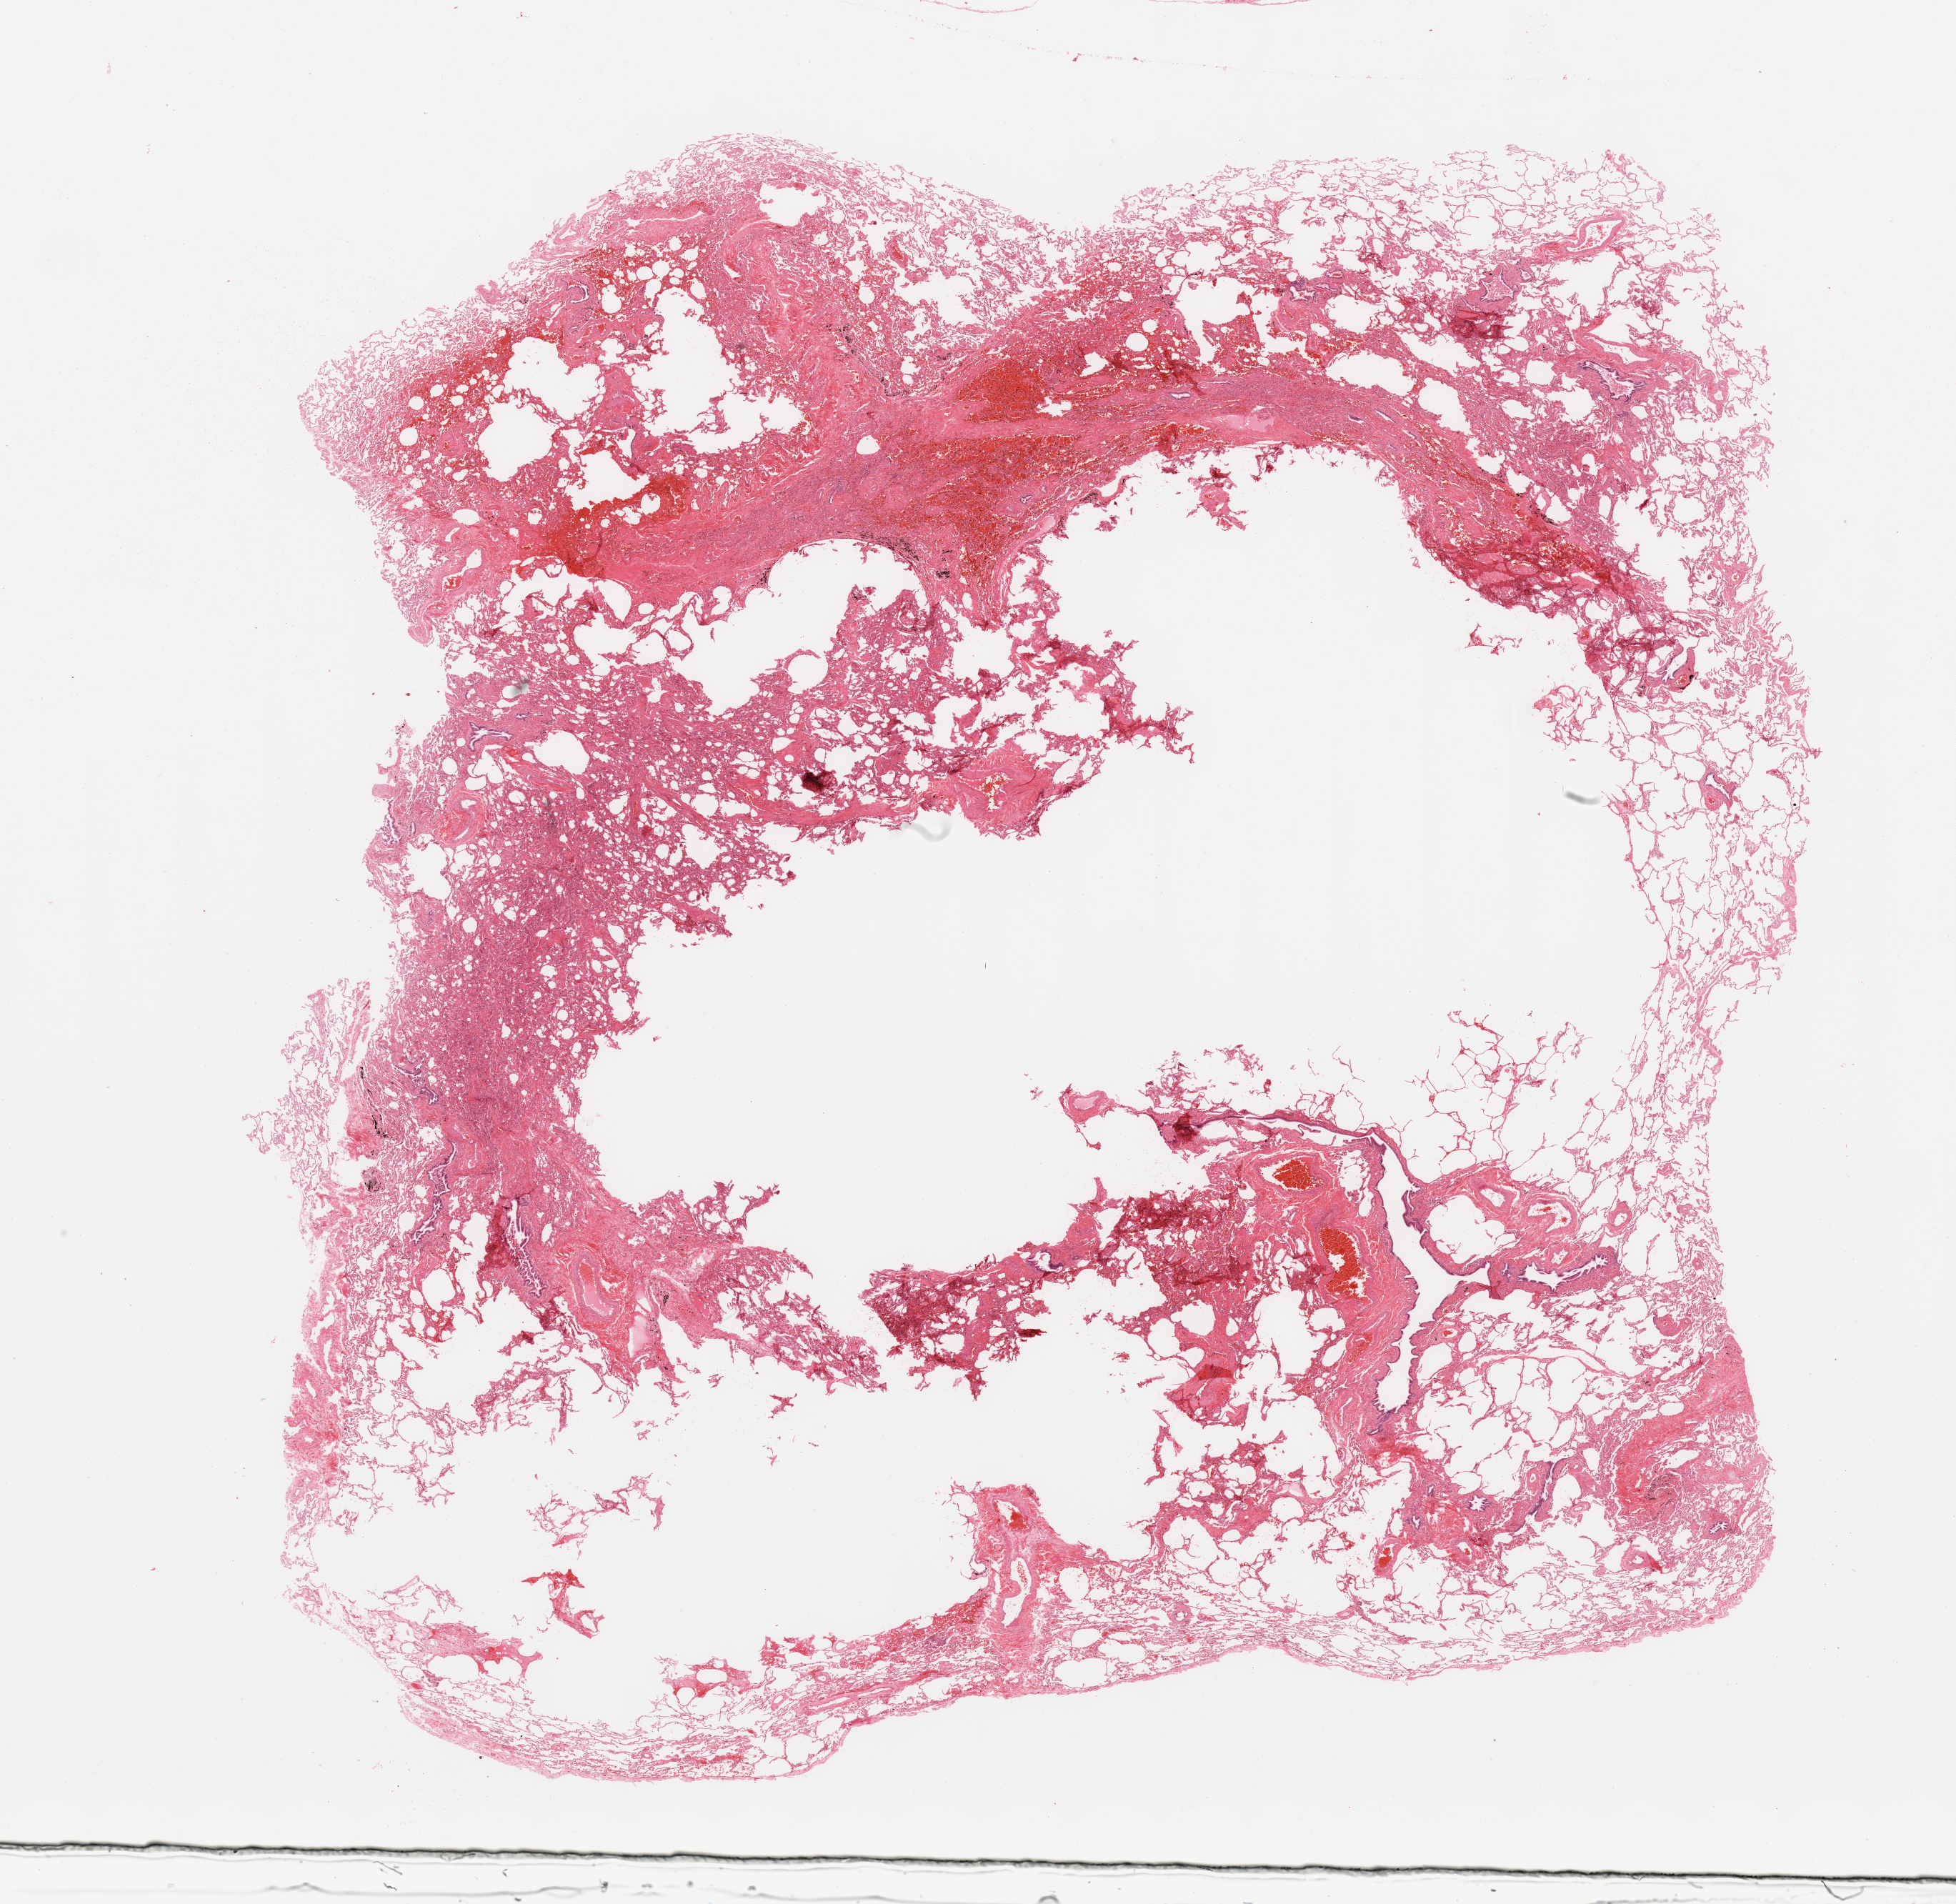
Whole-slide histology image, H&E — a low-resolution overview of the entire scanned area, about 21.7 x 21.1 mm (from a 20x scan); normal (non-tumour) tissue sample, sampled site: lung. Patient: male, age 64 years.
This section: normal (non-tumour) tissue from the same patient. Patient diagnosis: Adenocarcinoma, NOS.